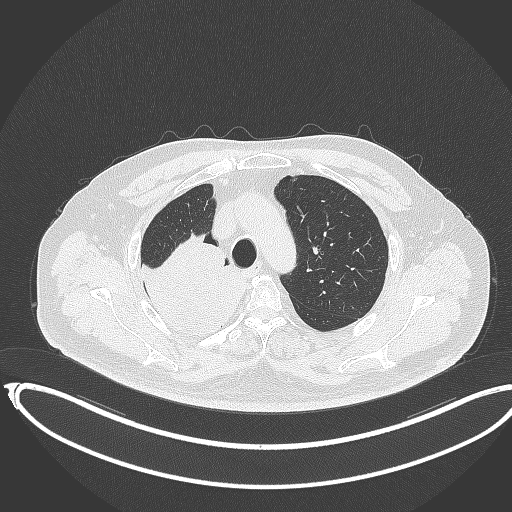
Chest CT, one axial slice; position 283 of 403 along the scan axis; reconstruction kernel B70f; lung window (W 1500 / L -600 HU); 512 × 512 image matrix. Male patient, age 68 years. From the clinical record (not read from this slice): clinical TNM (as recorded): T2a N0 M0.
Structures marked on this image (rectangle marked by the reading radiologist):
- lung tumour (recorded histology: adenocarcinoma): bounding box (x1, y1, x2, y2) in pixels: (135, 235, 248, 342)